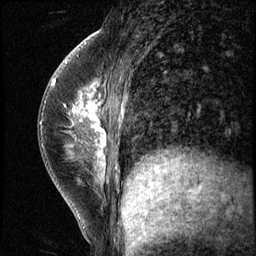
Breast MRI (dynamic contrast-enhanced), one sagittal slice. Slice 23 of 56 in the series (ordered by position). 3 images stored at this slice position (order not interpretable as contrast timing). 1.5 T. TE 4.2 ms, TR 8.7 ms. 2.5 mm slice thickness. 256 × 256 image matrix. Patient: female, 35 years. From the clinical record (not read from this slice): setting: breast cancer imaged before/during neoadjuvant chemotherapy; receptor status: HER2-positive.
Outlined on this slice (semi-automatic segmentation, software-assisted and operator-edited):
- analysis volume of interest (the breast-tissue region the enhancement analysis was run in; not a lesion): bounding box (x1, y1, x2, y2) in pixels: (58, 84, 138, 186)
- tumour enhancement mask (voxels above the 140 % enhancement threshold inside the analysis volume of interest): (74, 86, 124, 181)